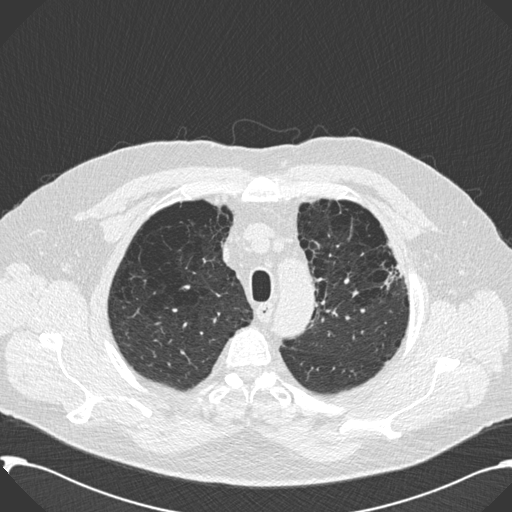
Chest CT (low-dose screening protocol), one axial image. Second annual screen. Lung window (W 1500 / L -600 HU). 2 mm slice thickness. Slice 34 of 199 in the series. Male, age 59 years at enrolment. Current smoker at enrolment.
• Expert reader's lesion annotation, bounding box (x1, y1, x2, y2) in pixels: (366, 239, 411, 304).
• No non-calcified nodule or mass ≥4 mm was recorded by the screening reader at this exam.
• Official screen result: negative screen, significant abnormalities not suspicious for lung cancer.
• Participant outcome: lung cancer diagnosed 518 days after this screen (after the third annual screen) — bronchiolo-alveolar carcinoma, mixed mucinous and non-mucinous, left upper lobe, stage IA (AJCC 6th edition), 20 mm at pathology.